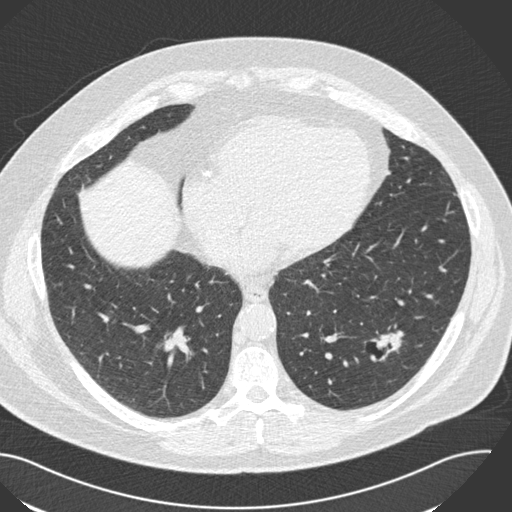
Axial slice from a low-dose chest CT screening exam, third annual screen, lung window (W 1500 / L -600 HU), 2 mm slice thickness, standard (soft-tissue) reconstruction kernel (B30f). Male participant, aged 57 years at enrolment. Current smoker at enrolment.
• Expert-annotated lung lesion, box from (x=349, y=317) to (x=422, y=376) px.
• Screening reader's record for this exam (one nodule recorded; not confirmed to be the boxed lesion): non-calcified nodule or mass ≥4 mm, left lower lobe, 22 × 18 mm, poorly defined margins, soft tissue attenuation, pre-existing on the prior screen: yes; interval growth: yes.
• Official screen result: positive, other.
• Lung cancer was diagnosed 124 days after this screen: squamous cell carcinoma, NOS, left lower lobe, moderately differentiated (G2), stage IA (AJCC 6th edition), 22 mm at pathology.